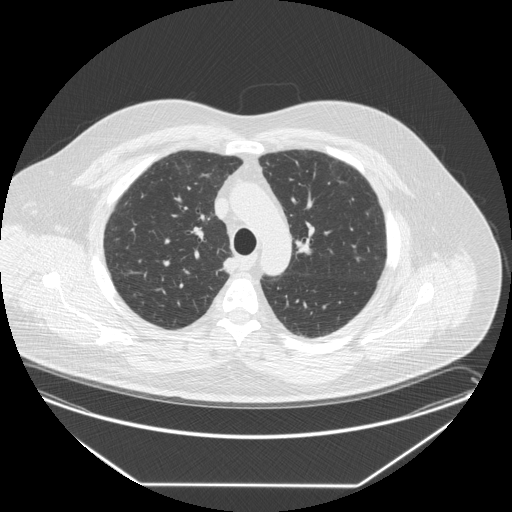
Axial slice from a low-dose chest CT screening exam; third annual screen; lung window (W 1500 / L -600 HU); 2.5 mm slice thickness; slice 61 of 258 in the series. Male, age 58 years at enrolment.
Lesion marked by an expert reader, bounding box <212,253,242,279> (left, top, right, bottom; pixels). Screening reader's record for this exam (one nodule recorded; not confirmed to be the boxed lesion): non-calcified nodule or mass ≥4 mm, right upper lobe, 15 × 12 mm, smooth margins, soft tissue attenuation, pre-existing on the prior screen: no. Official screen result: positive, other. Participant outcome: lung cancer diagnosed 17 days after this screen — large cell carcinoma, NOS, right upper lobe, stage IV (AJCC 6th edition), 35 mm at pathology.